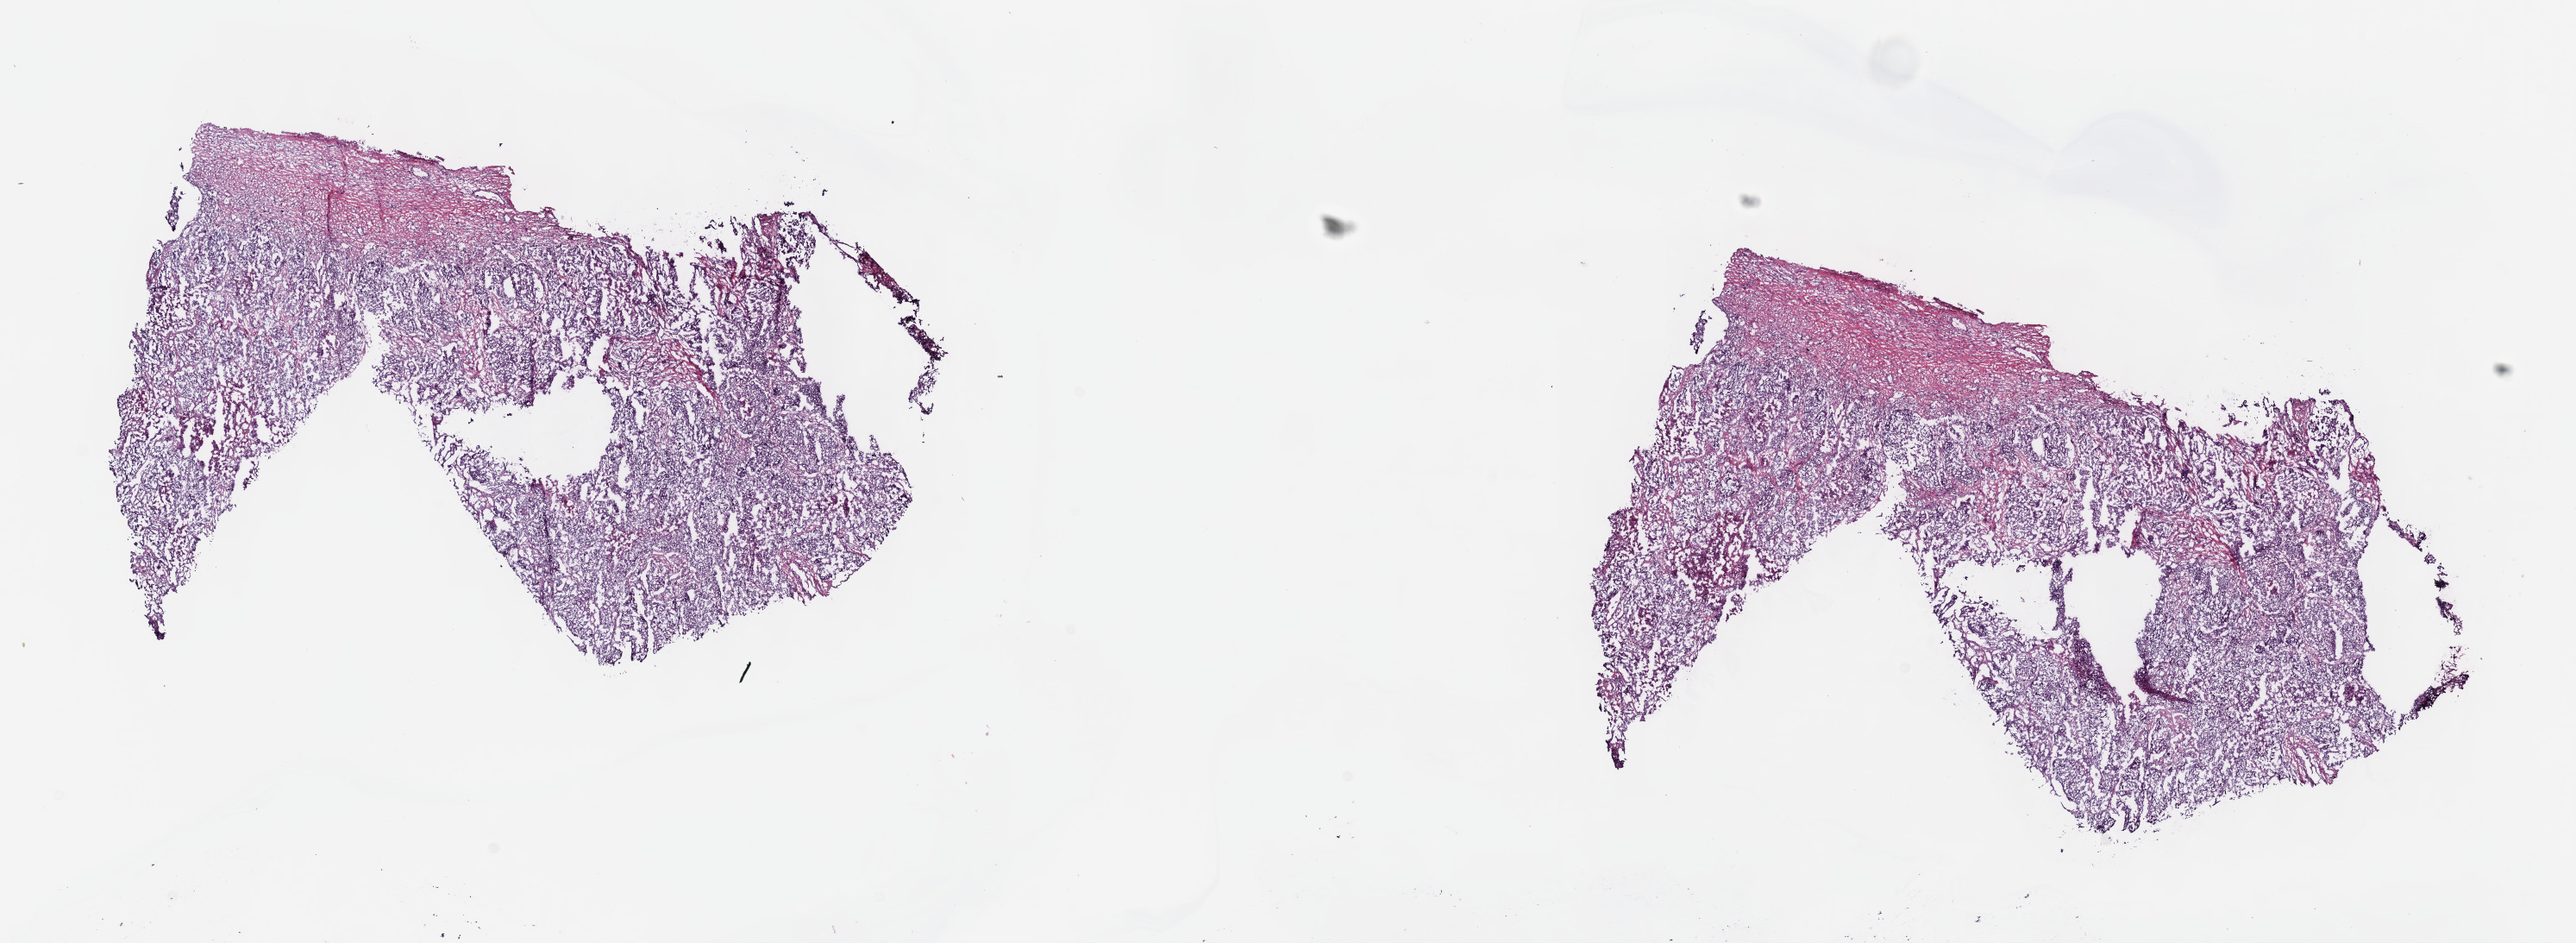
H&E-stained whole-slide image — a low-resolution overview of the entire scanned area, about 24.2 x 8.8 mm, frozen section from the top of the tissue portion, lung, primary tumour sample. Patient: male, age at initial diagnosis 66 years. Composition of this section per pathologist review: tumour cells 80%, tumour nuclei 80%, normal cells 0%, stromal cells 15%, necrosis 5%. Infiltration values recorded for this section: lymphocyte infiltration 40%, monocyte infiltration 20%, neutrophil infiltration 20%.
Pathologic diagnosis: Squamous cell carcinoma, NOS (upper lobe, lung). AJCC pathologic stage: IIIB (7th edition).